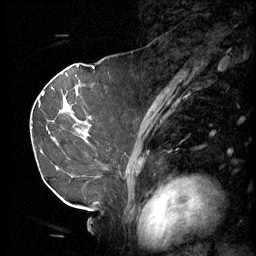
Breast MRI (dynamic contrast-enhanced), one sagittal slice. Slice 32 of 60 in the series (ordered by position). 3 images stored at this slice position (order not interpretable as contrast timing). 1.5 T. TE 4.2 ms, TR 11 ms. 256 × 256 image matrix. Patient: female, 69 years.
Annotated regions visible in this slice (semi-automatically segmented with operator editing):
- analysis volume of interest (the breast-tissue region the enhancement analysis was run in; not a lesion): bounding box <36,88,110,189> (left, top, right, bottom; pixels)
- tumour enhancement mask (voxels above the 70 % enhancement threshold inside the analysis volume of interest): <63,98,88,131>